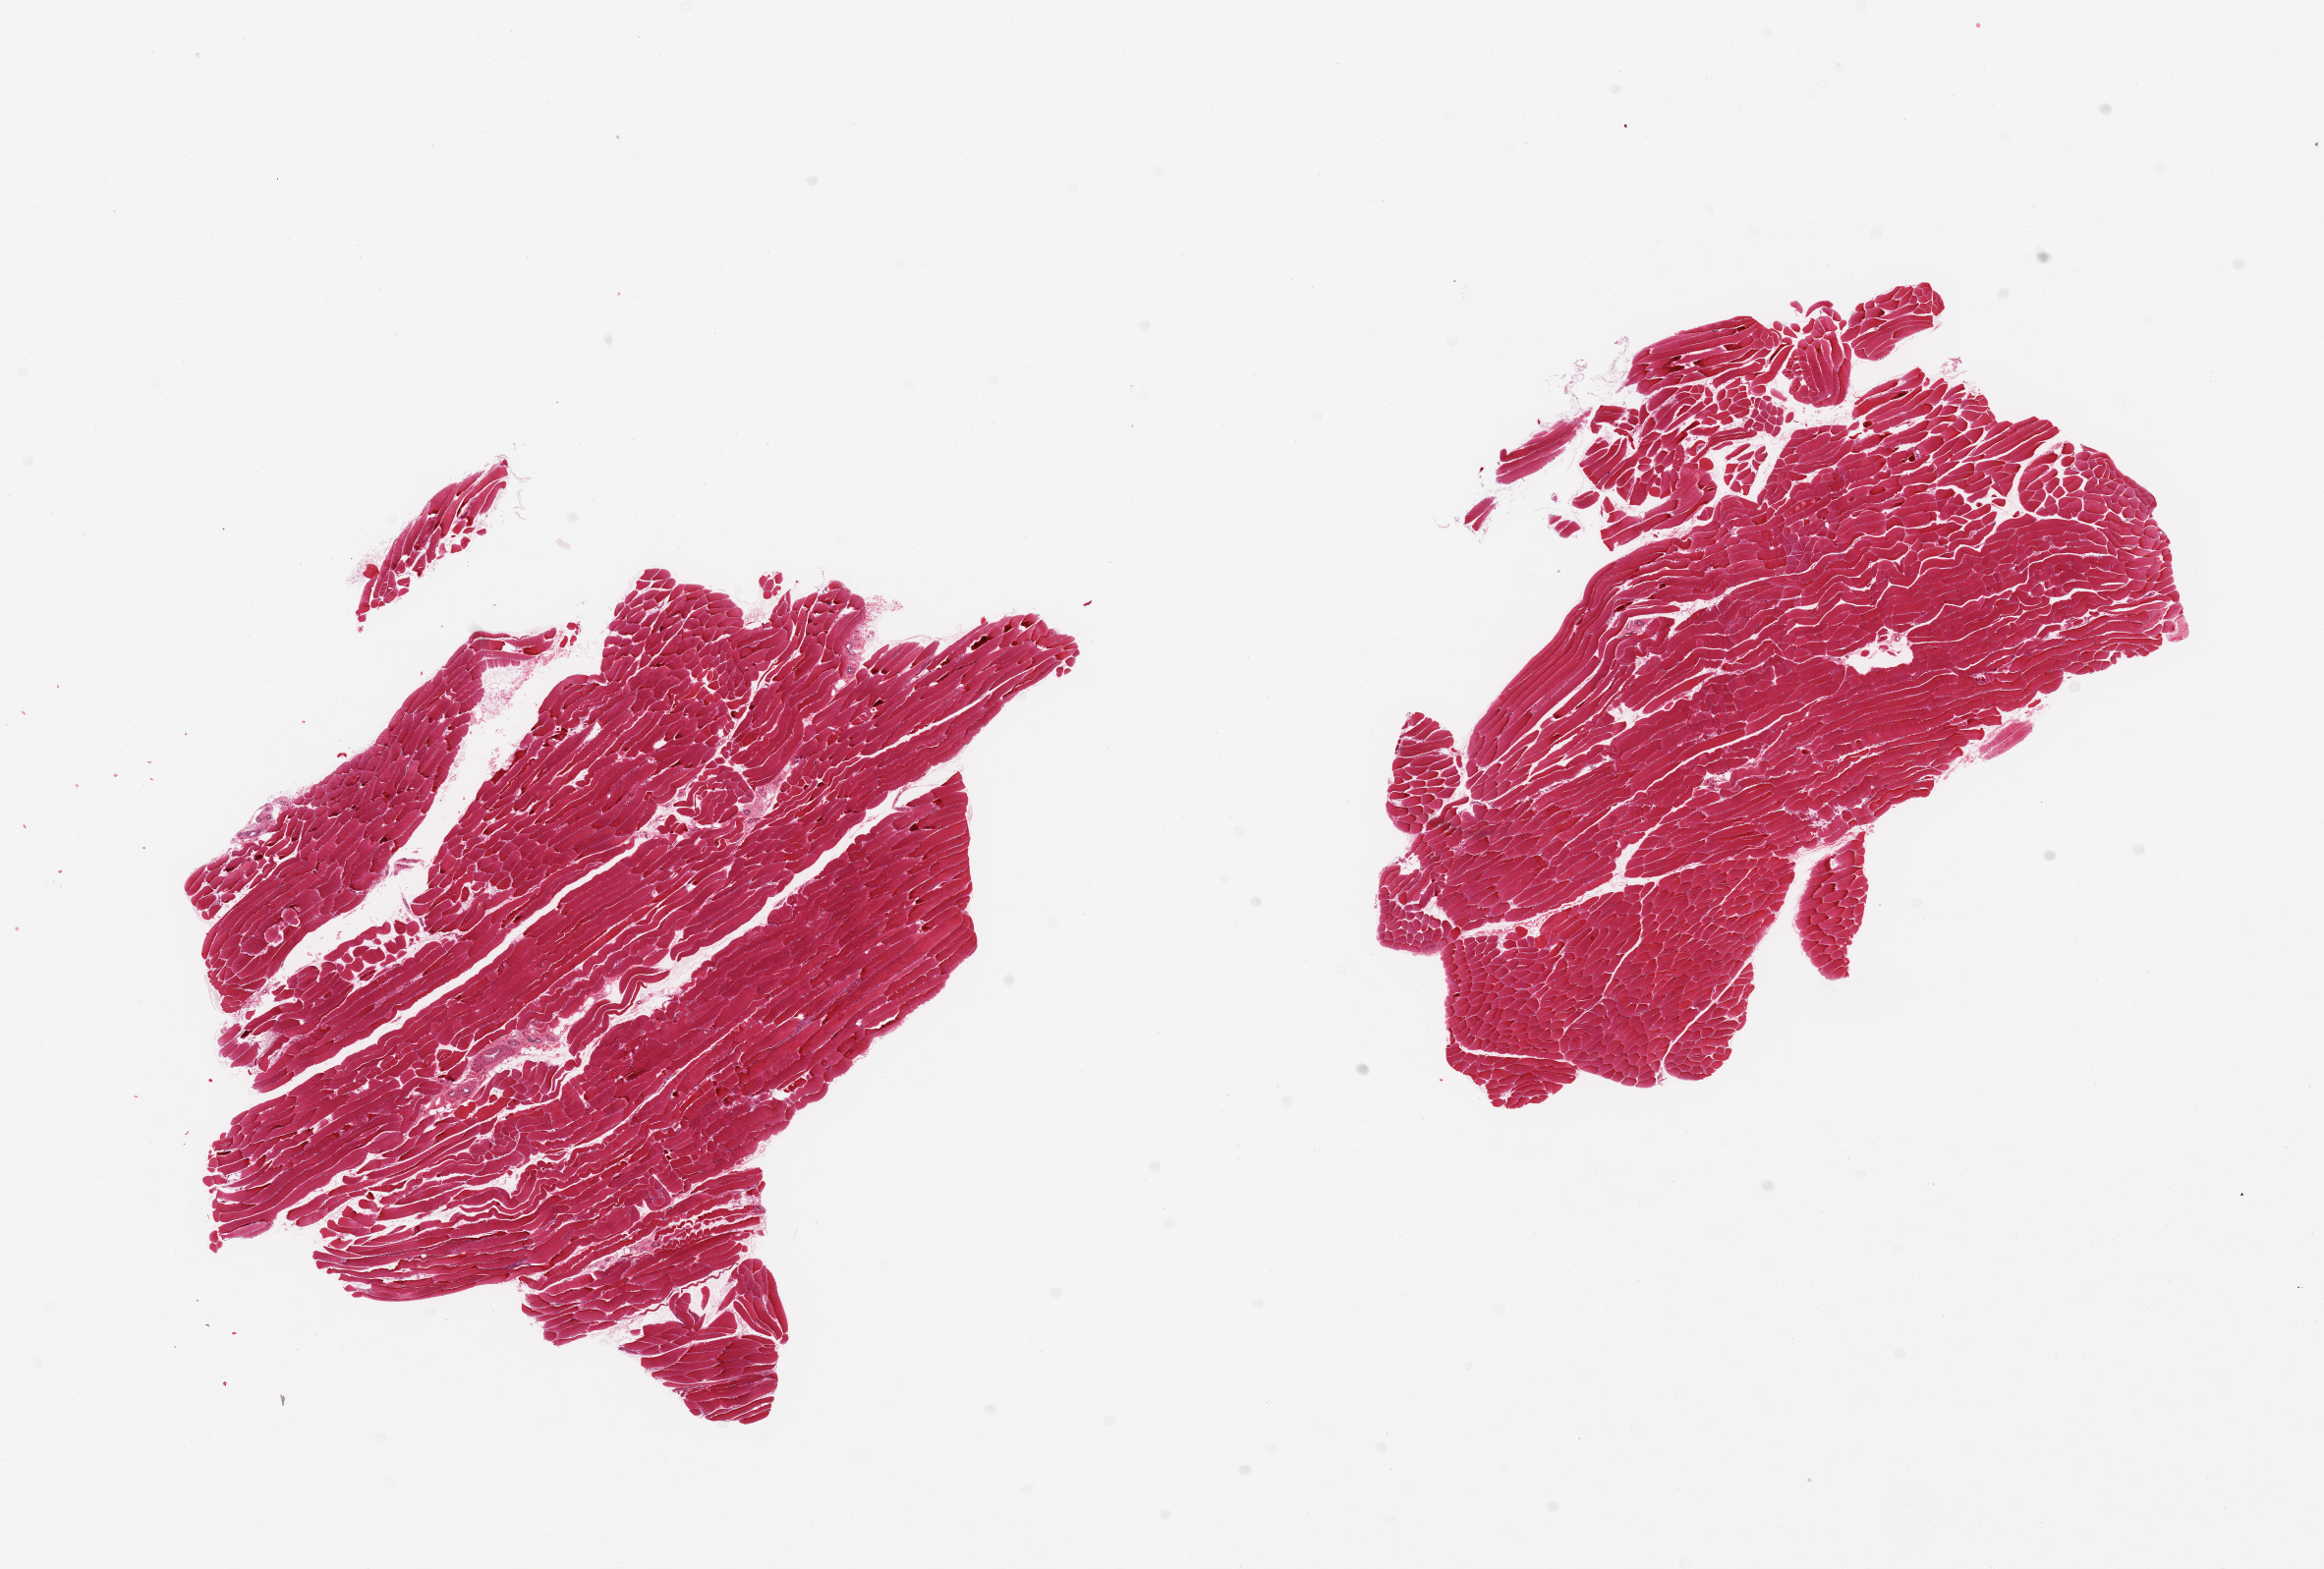
Whole-slide image, H&E stain, brightfield — whole scanned area (about 18.7 x 12.6 mm, slide scanned at 20x) shown as a low-resolution overview; PAXgene-fixed, paraffin-embedded tissue; sampled site (target tissue): skeletal muscle; tissue donor sample. Donor: male.
• reviewer comment on this tissue sample: 2 pieces, minimal interstitial fat